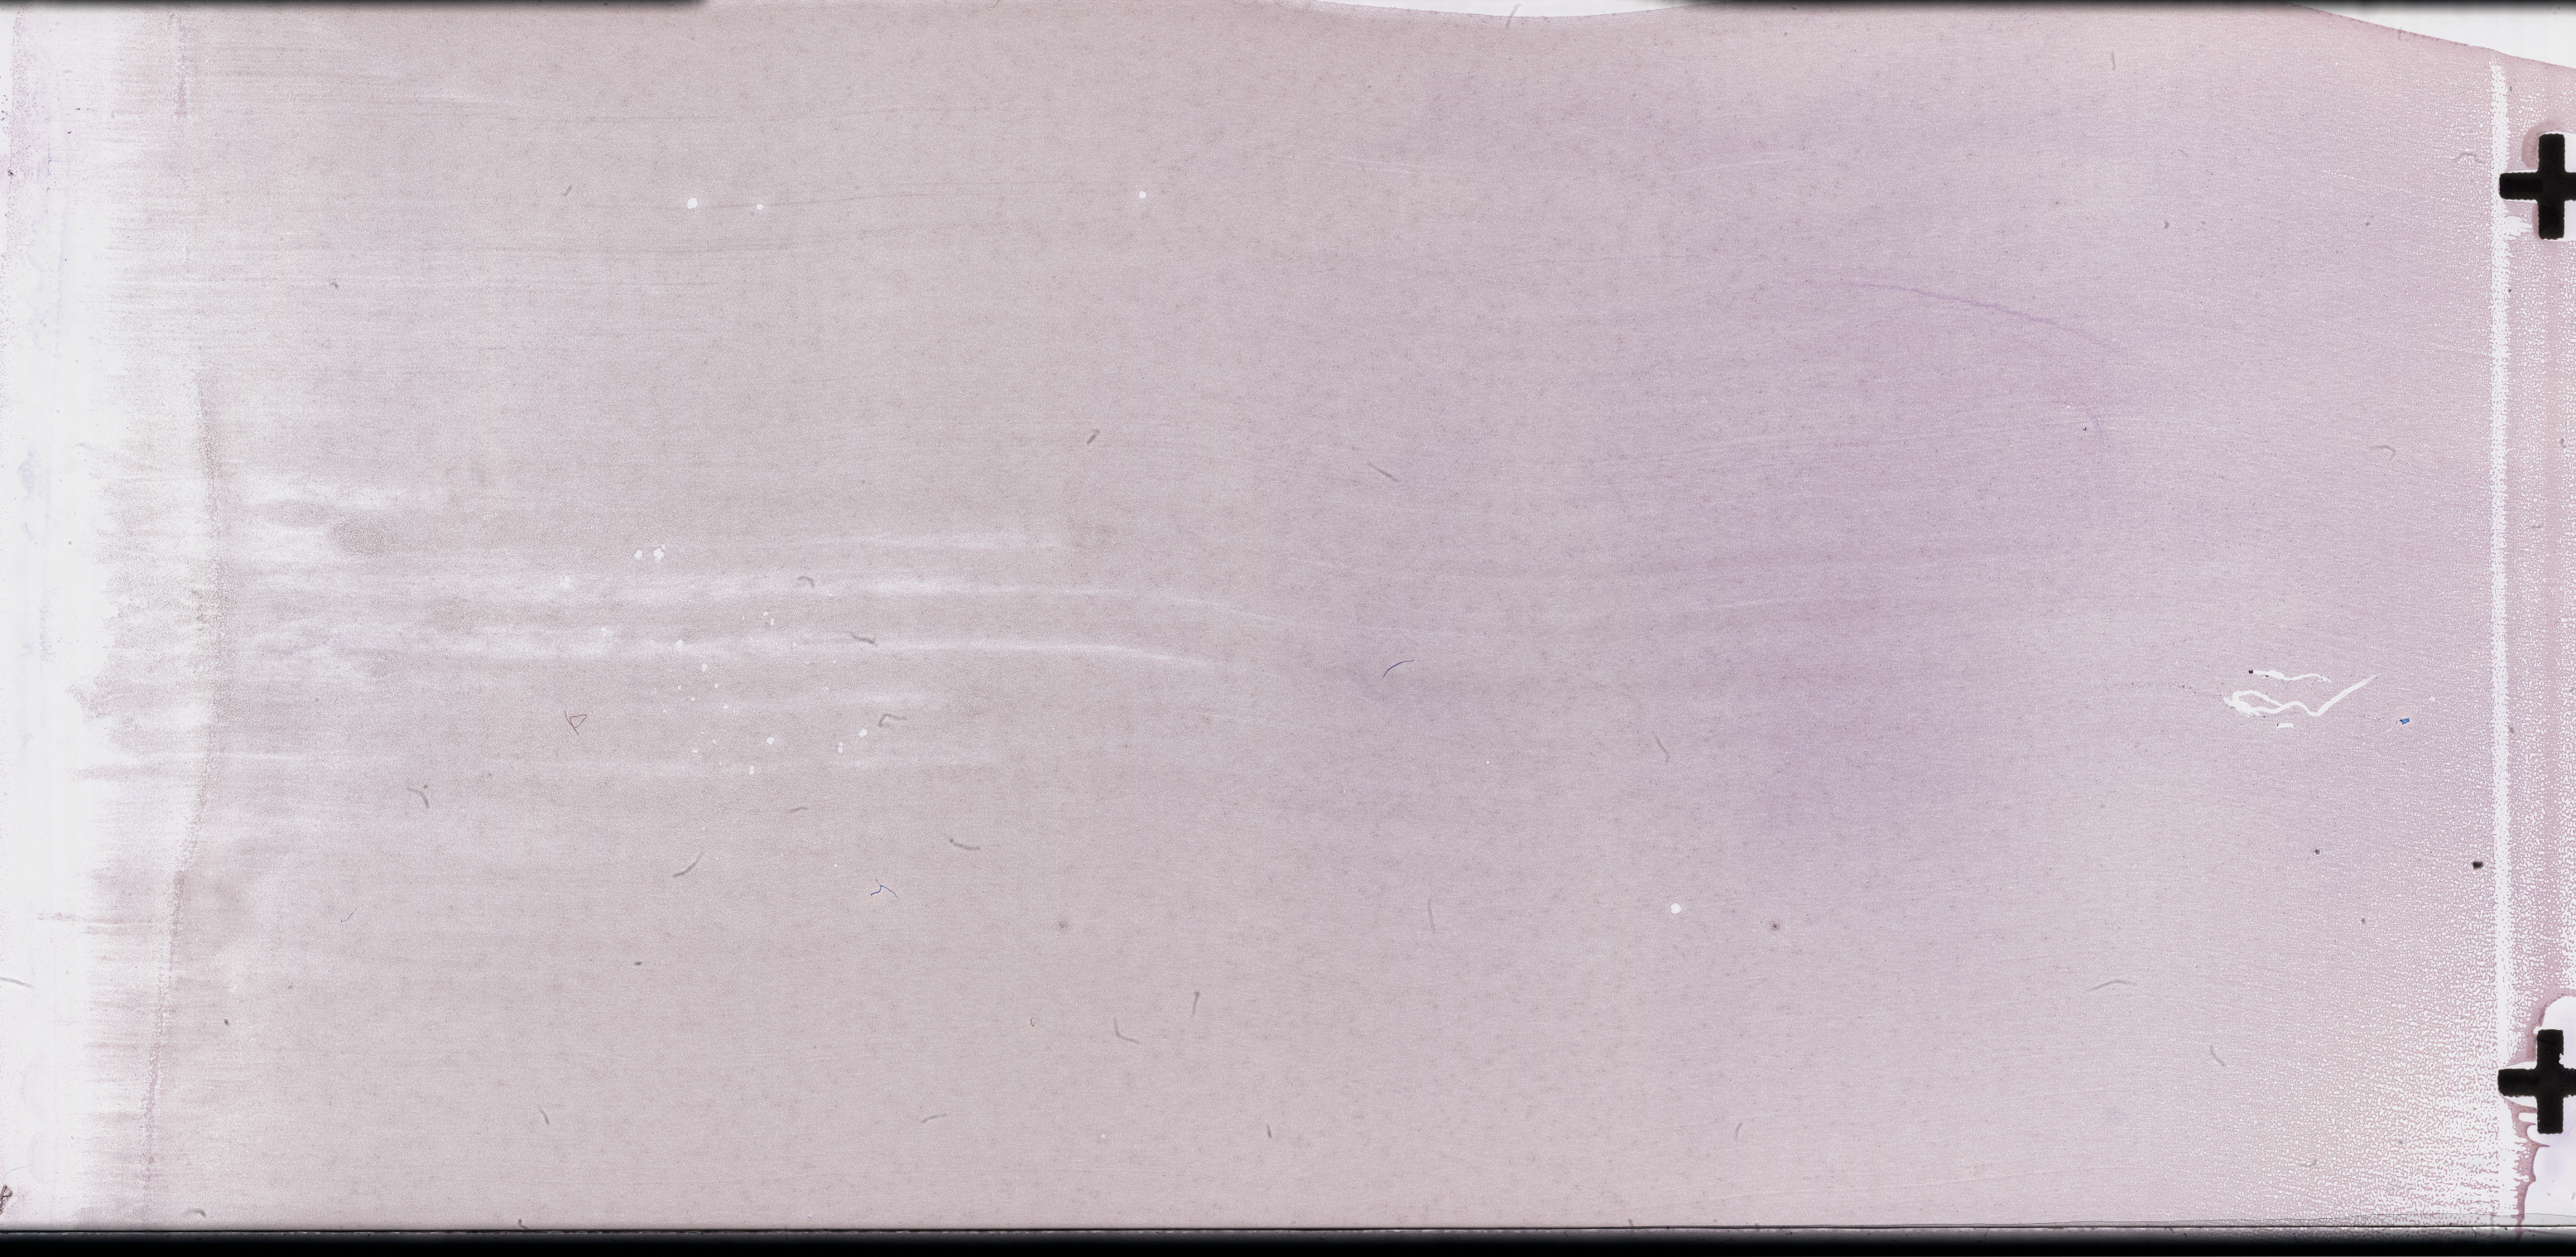
Wright–Giemsa-stained whole blood smear, whole-slide image, low-resolution overview of the scanned area, about 50.3 x 24.5 mm; EDTA-anticoagulated smear; collected on treatment. Patient sex: male.
Patient diagnosis: Plasma Cell Myeloma.